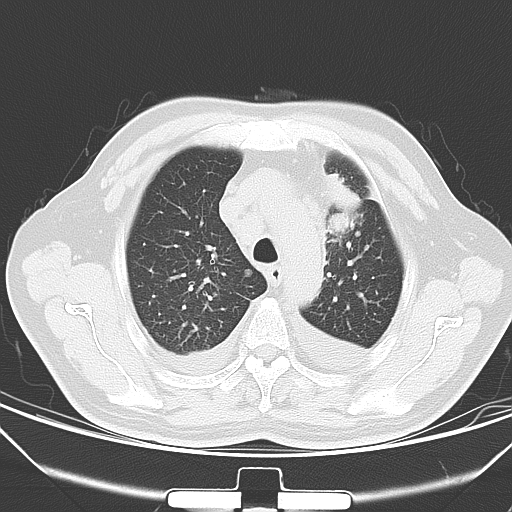
Chest CT, one axial slice. Position 49 of 66 along the scan axis. Lung window (W 1500 / L -600 HU). 5 mm slice thickness. 512 × 512 image matrix, field of view 352 × 352 mm. Patient: male, 66 years. Case-level facts recorded for this patient, not image findings: clinical TNM (as recorded): T1c N0 M0.
Structures marked on this image (bounding box drawn by a radiologist):
- lung tumour (recorded histology: adenocarcinoma): bounding box (x1, y1, x2, y2) in pixels: (324, 170, 362, 238)